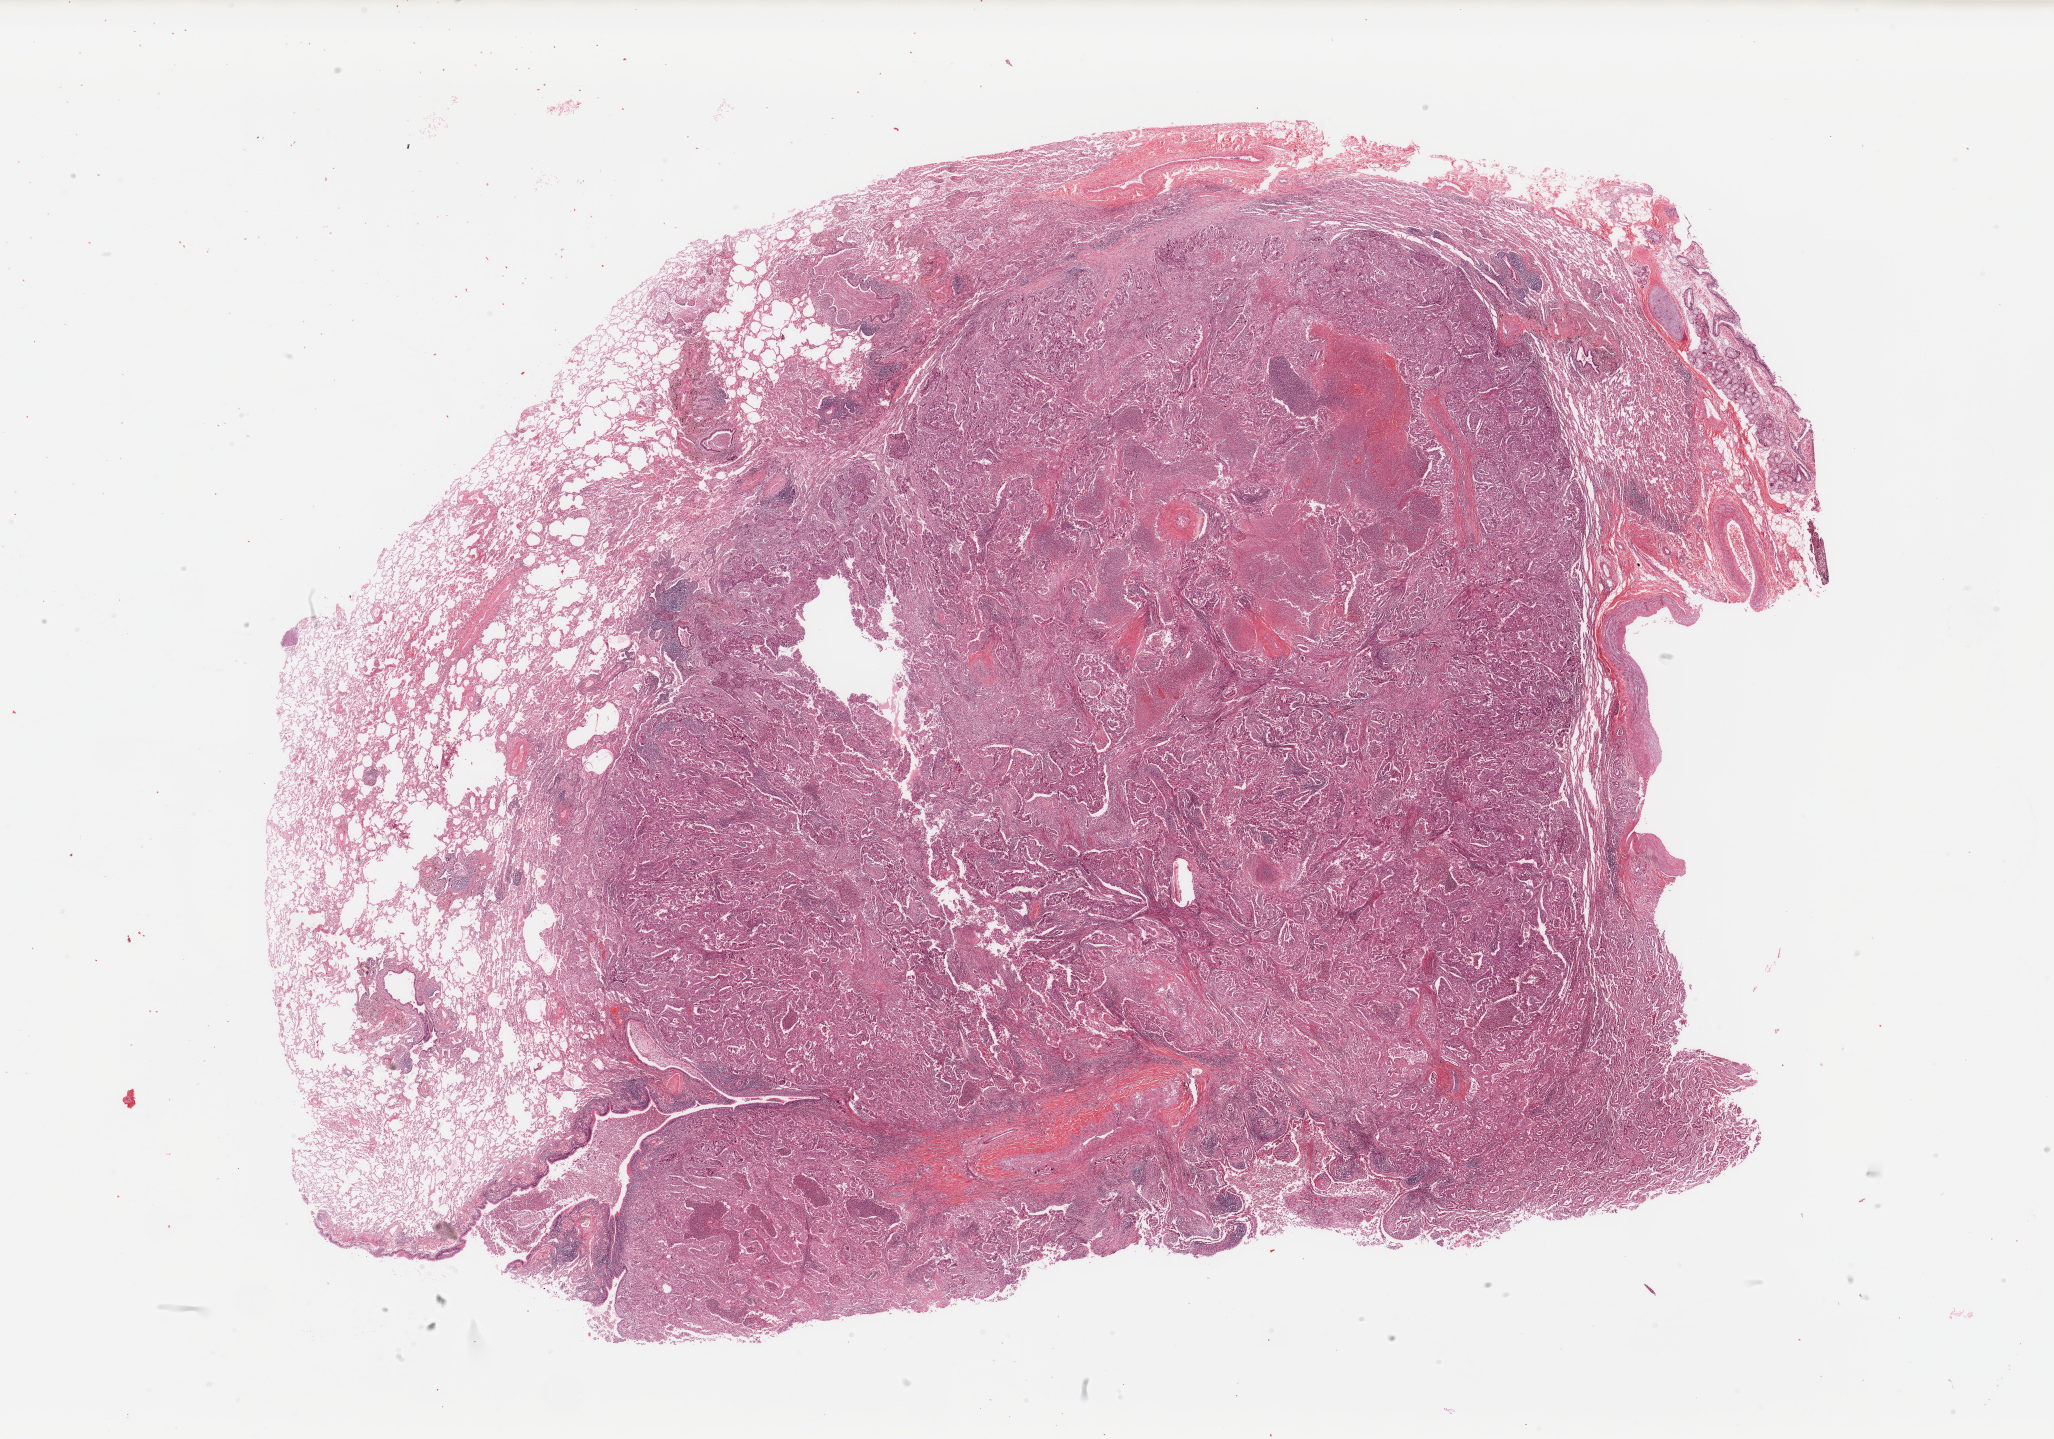
H&E whole-slide image, low-resolution overview of the scanned area, about 32.5 x 22.8 mm, lung, tumour tissue. 61-year-old female patient. Histologic grade: G3 (poorly differentiated).
• AJCC pathologic stage: IIIA
• diagnosis: Adenocarcinoma, NOS